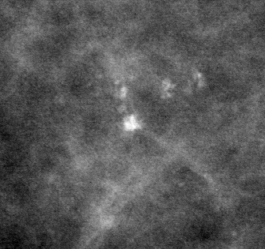
Region of interest cut from a scanned film mammogram (one marked finding), left breast, CC view.
Marked abnormality: calcifications, morphology pleomorphic, distribution clustered; BI-RADS assessment category 4; subtlety rating 5 on a 1 (subtle) to 5 (obvious) scale; pathology result (as recorded, not read from the image): benign.